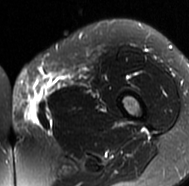
MRI of an extremity soft-tissue mass, one axial slice; slice 23 of 77 in the series (ordered by position); T2-weighted fat-saturated; MR volume resampled by the dataset authors to the PET/CT grid (not the native acquisition matrix); 3.27 mm slice thickness; 189 × 186 image matrix, field of view 185 × 182 mm. Female patient. Case-level facts recorded for this patient, not image findings: histological type: leiomyosarcoma; grade: high; site of the primary tumour: groin.
Structures marked on this image (expert contour drawn on MRI and transferred to this co-registered scan by the dataset authors):
- gross tumour volume including surrounding oedema: box from (x=12, y=65) to (x=94, y=133) px